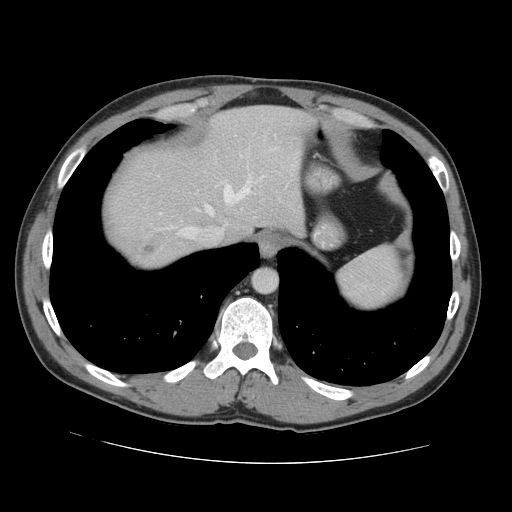
Contrast-enhanced abdominal CT, one axial slice; position 119 of 131 along the scan axis; 120 kVp; intravenous contrast given; soft-tissue window (W 400 / L 40 HU); 2.5 mm slice thickness; 512 × 512 image matrix, field of view 380 × 380 mm. Male patient, age 40 years. Case-level facts recorded for this patient, not image findings: diagnosis: colorectal cancer liver metastases, imaged before liver resection.
Structures marked on this image (expert manual segmentation):
- hepatic veins: bounding box <180,181,250,237> (left, top, right, bottom; pixels)
- liver: <108,107,310,267>
- planned liver remnant (the part of the liver to remain after resection): <127,107,310,239>
- liver metastasis: <145,246,154,254>